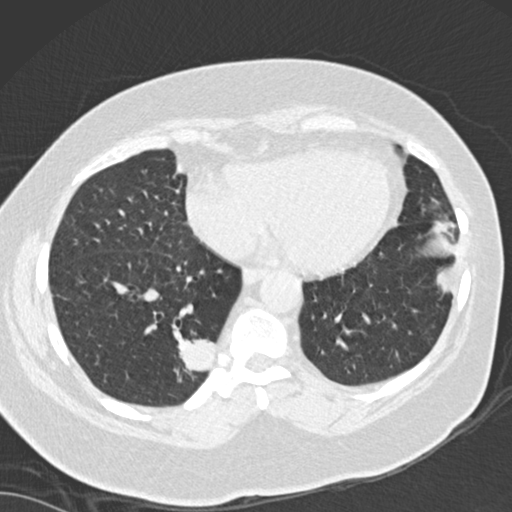
Axial slice from a low-dose chest CT screening exam. Baseline annual screen. Lung window (W 1500 / L -600 HU). 2 mm slice thickness. 120 kVp. Slice 109 of 162 in the series. 512 × 512 image matrix, field of view 328 × 328 mm. Female participant, aged 66 years at enrolment. Current smoker at enrolment.
• Expert-annotated lung lesion, box from (x=144, y=313) to (x=236, y=408) px.
• The screening reader recorded 3 non-calcified nodules or masses ≥4 mm on this exam (left lower lobe, left lower lobe, right lower lobe); which of them this box marks is not recorded.
• Official screen result: positive, change unspecified: nodule(s) >= 4 mm or enlarging nodule(s), mass(es), or other non-specific abnormalities suspicious for lung cancer.
• Later outcome: lung cancer diagnosed 67 days after this screen — adenocarcinoma, NOS, right lower lobe, well differentiated (G1), stage IB (AJCC 6th edition), 55 mm at pathology.